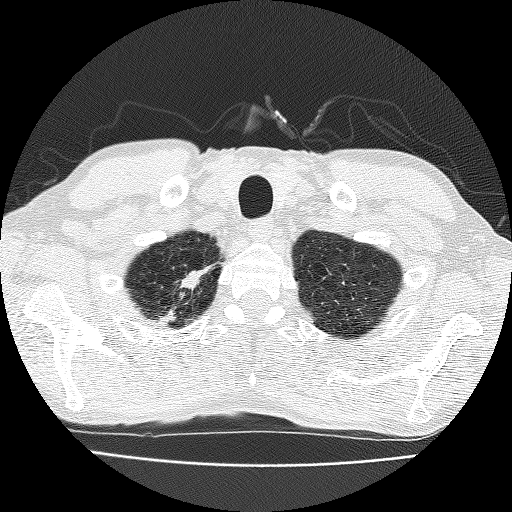
Chest CT (low-dose screening protocol), one axial image; third annual screen; lung window (W 1500 / L -600 HU); 512 × 512 image matrix. Male, age 63 years at enrolment.
Expert-annotated lung lesion, box from (x=146, y=258) to (x=226, y=328) px. Screening reader's record for this exam (one nodule recorded; not confirmed to be the boxed lesion): non-calcified nodule or mass ≥4 mm, right upper lobe, 17 × 10 mm, spiculated (stellate) margins, soft tissue attenuation, pre-existing on the prior screen: yes; interval growth: yes. Official screen result: positive, other.